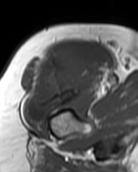
MRI of an extremity soft-tissue mass, one axial slice. MR volume resampled by the dataset authors to the PET/CT grid (not the native acquisition matrix). 3.27 mm slice thickness. 138 × 172 image matrix. Female patient. Case-level facts recorded for this patient, not image findings: histological type: pleiomorphic undifferentiated sarcoma; grade: high; site of the primary tumour: right quadricep.
Annotated regions visible in this slice (expert contour drawn on MRI and transferred to this co-registered scan by the dataset authors):
- gross tumour volume including surrounding oedema: bounding box [x1, y1, x2, y2] px = [23, 46, 97, 122]
- gross tumour volume (mass): [23, 46, 97, 122]